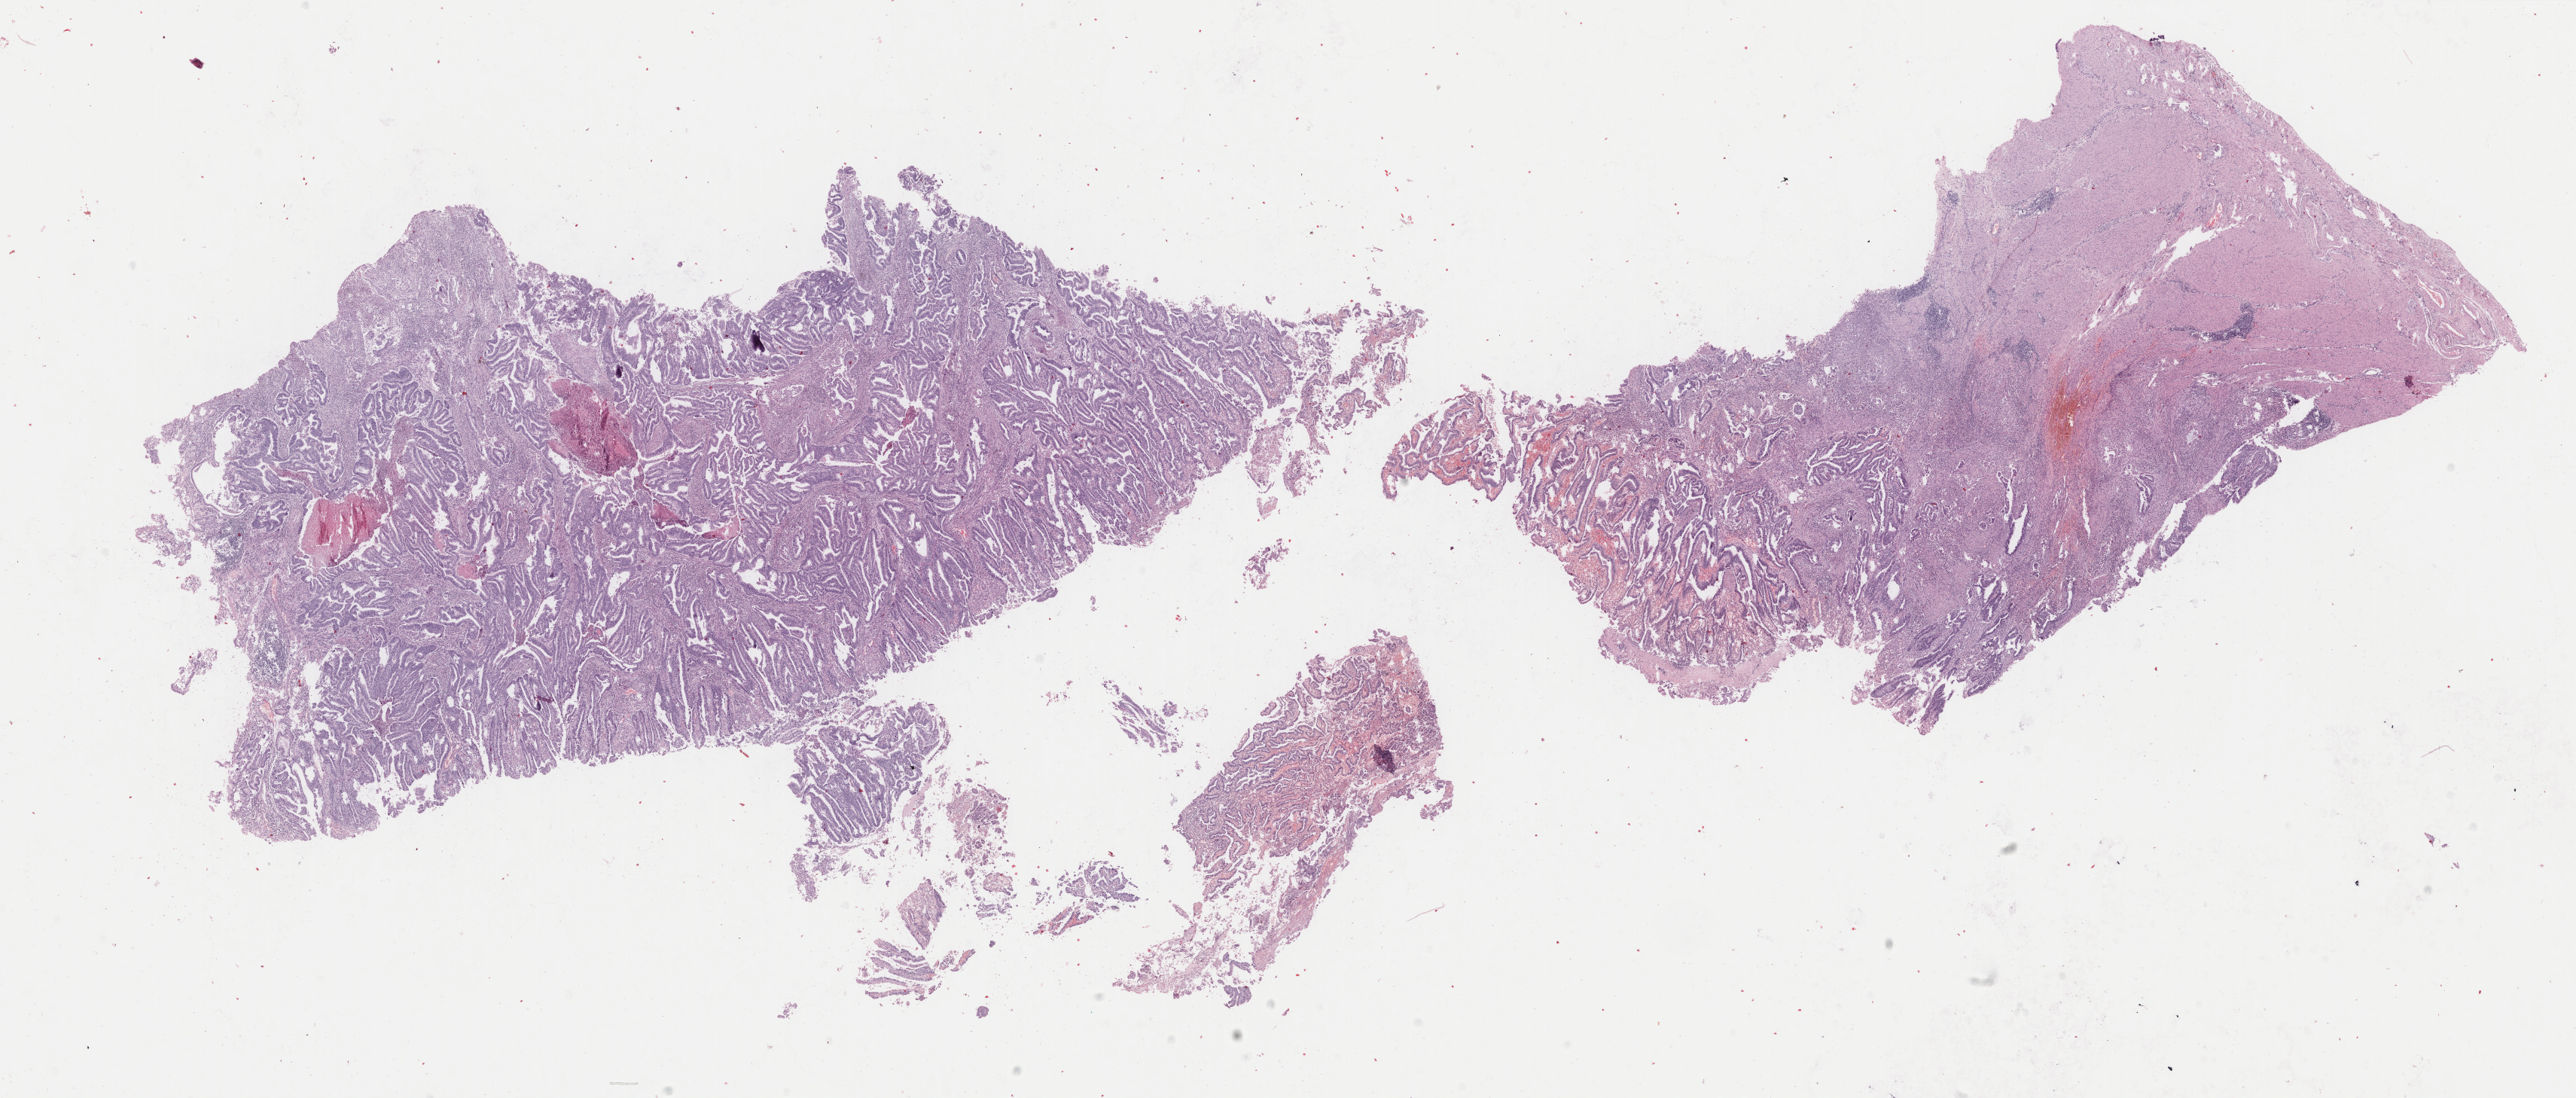
Whole-slide histology image, H&E — whole scanned area (about 27.2 x 11.6 mm, from a 40x scan) shown as a low-resolution overview, formalin-fixed paraffin-embedded (FFPE) diagnostic section, stomach, primary tumour sample. Male patient; age at initial diagnosis 57 years. Histologic grade: G2 (moderately differentiated).
AJCC pathologic stage: IIB. Pathologic diagnosis: Adenocarcinoma, NOS (fundus of stomach).